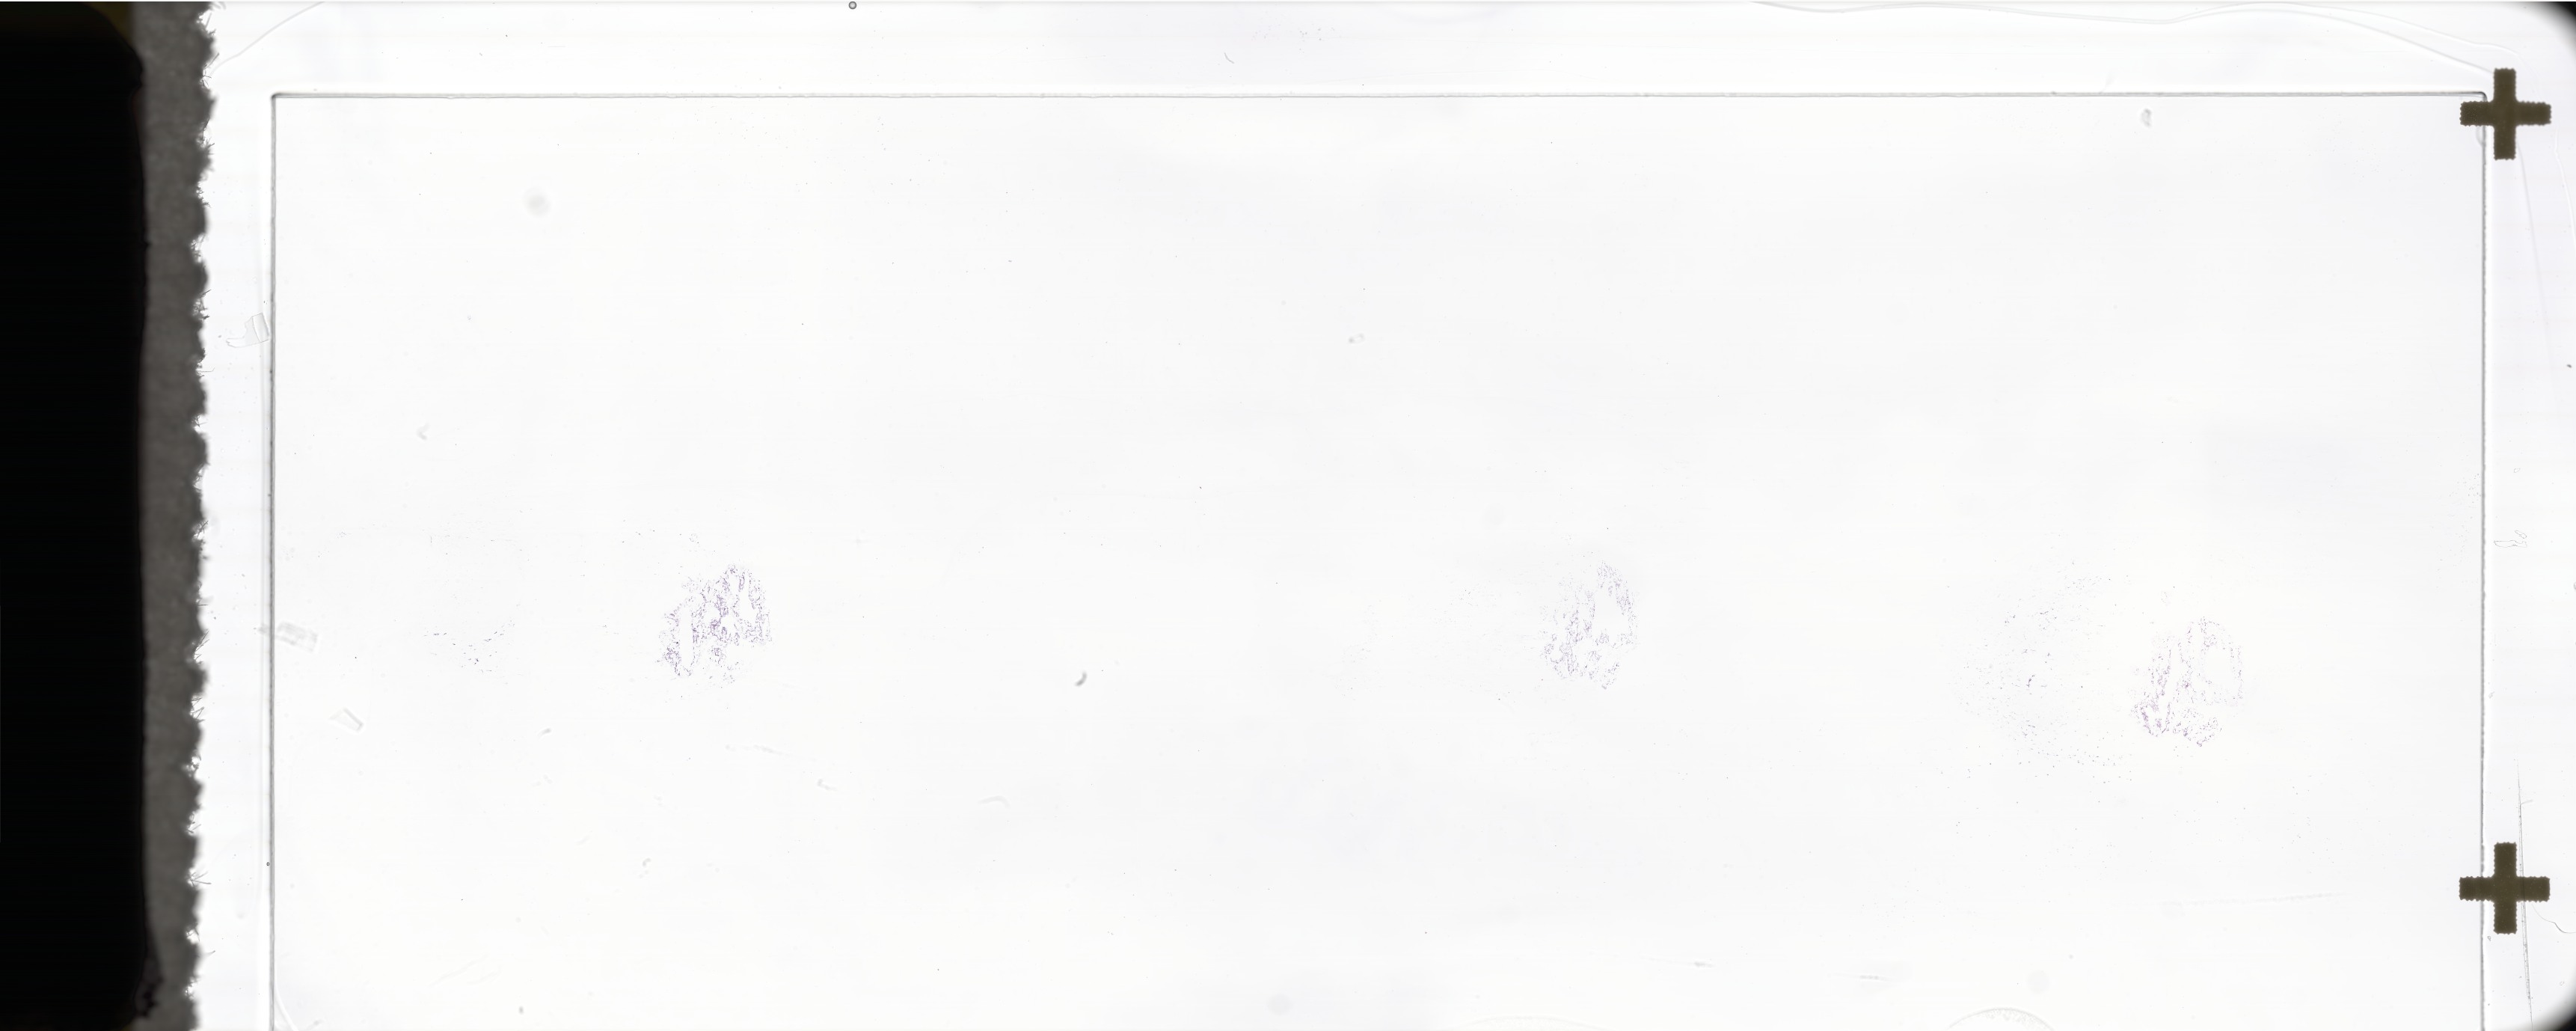
Haematoxylin and eosin whole-slide image of tumor tissue from the brain, a low-resolution overview of the entire scanned area, about 58.1 x 23.2 mm; frozen section (OCT-embedded). Patient: male, age 195 months (16 years 3 months).
Diagnosis (ICD-O-3 morphology term): Neoplasm, malignant.